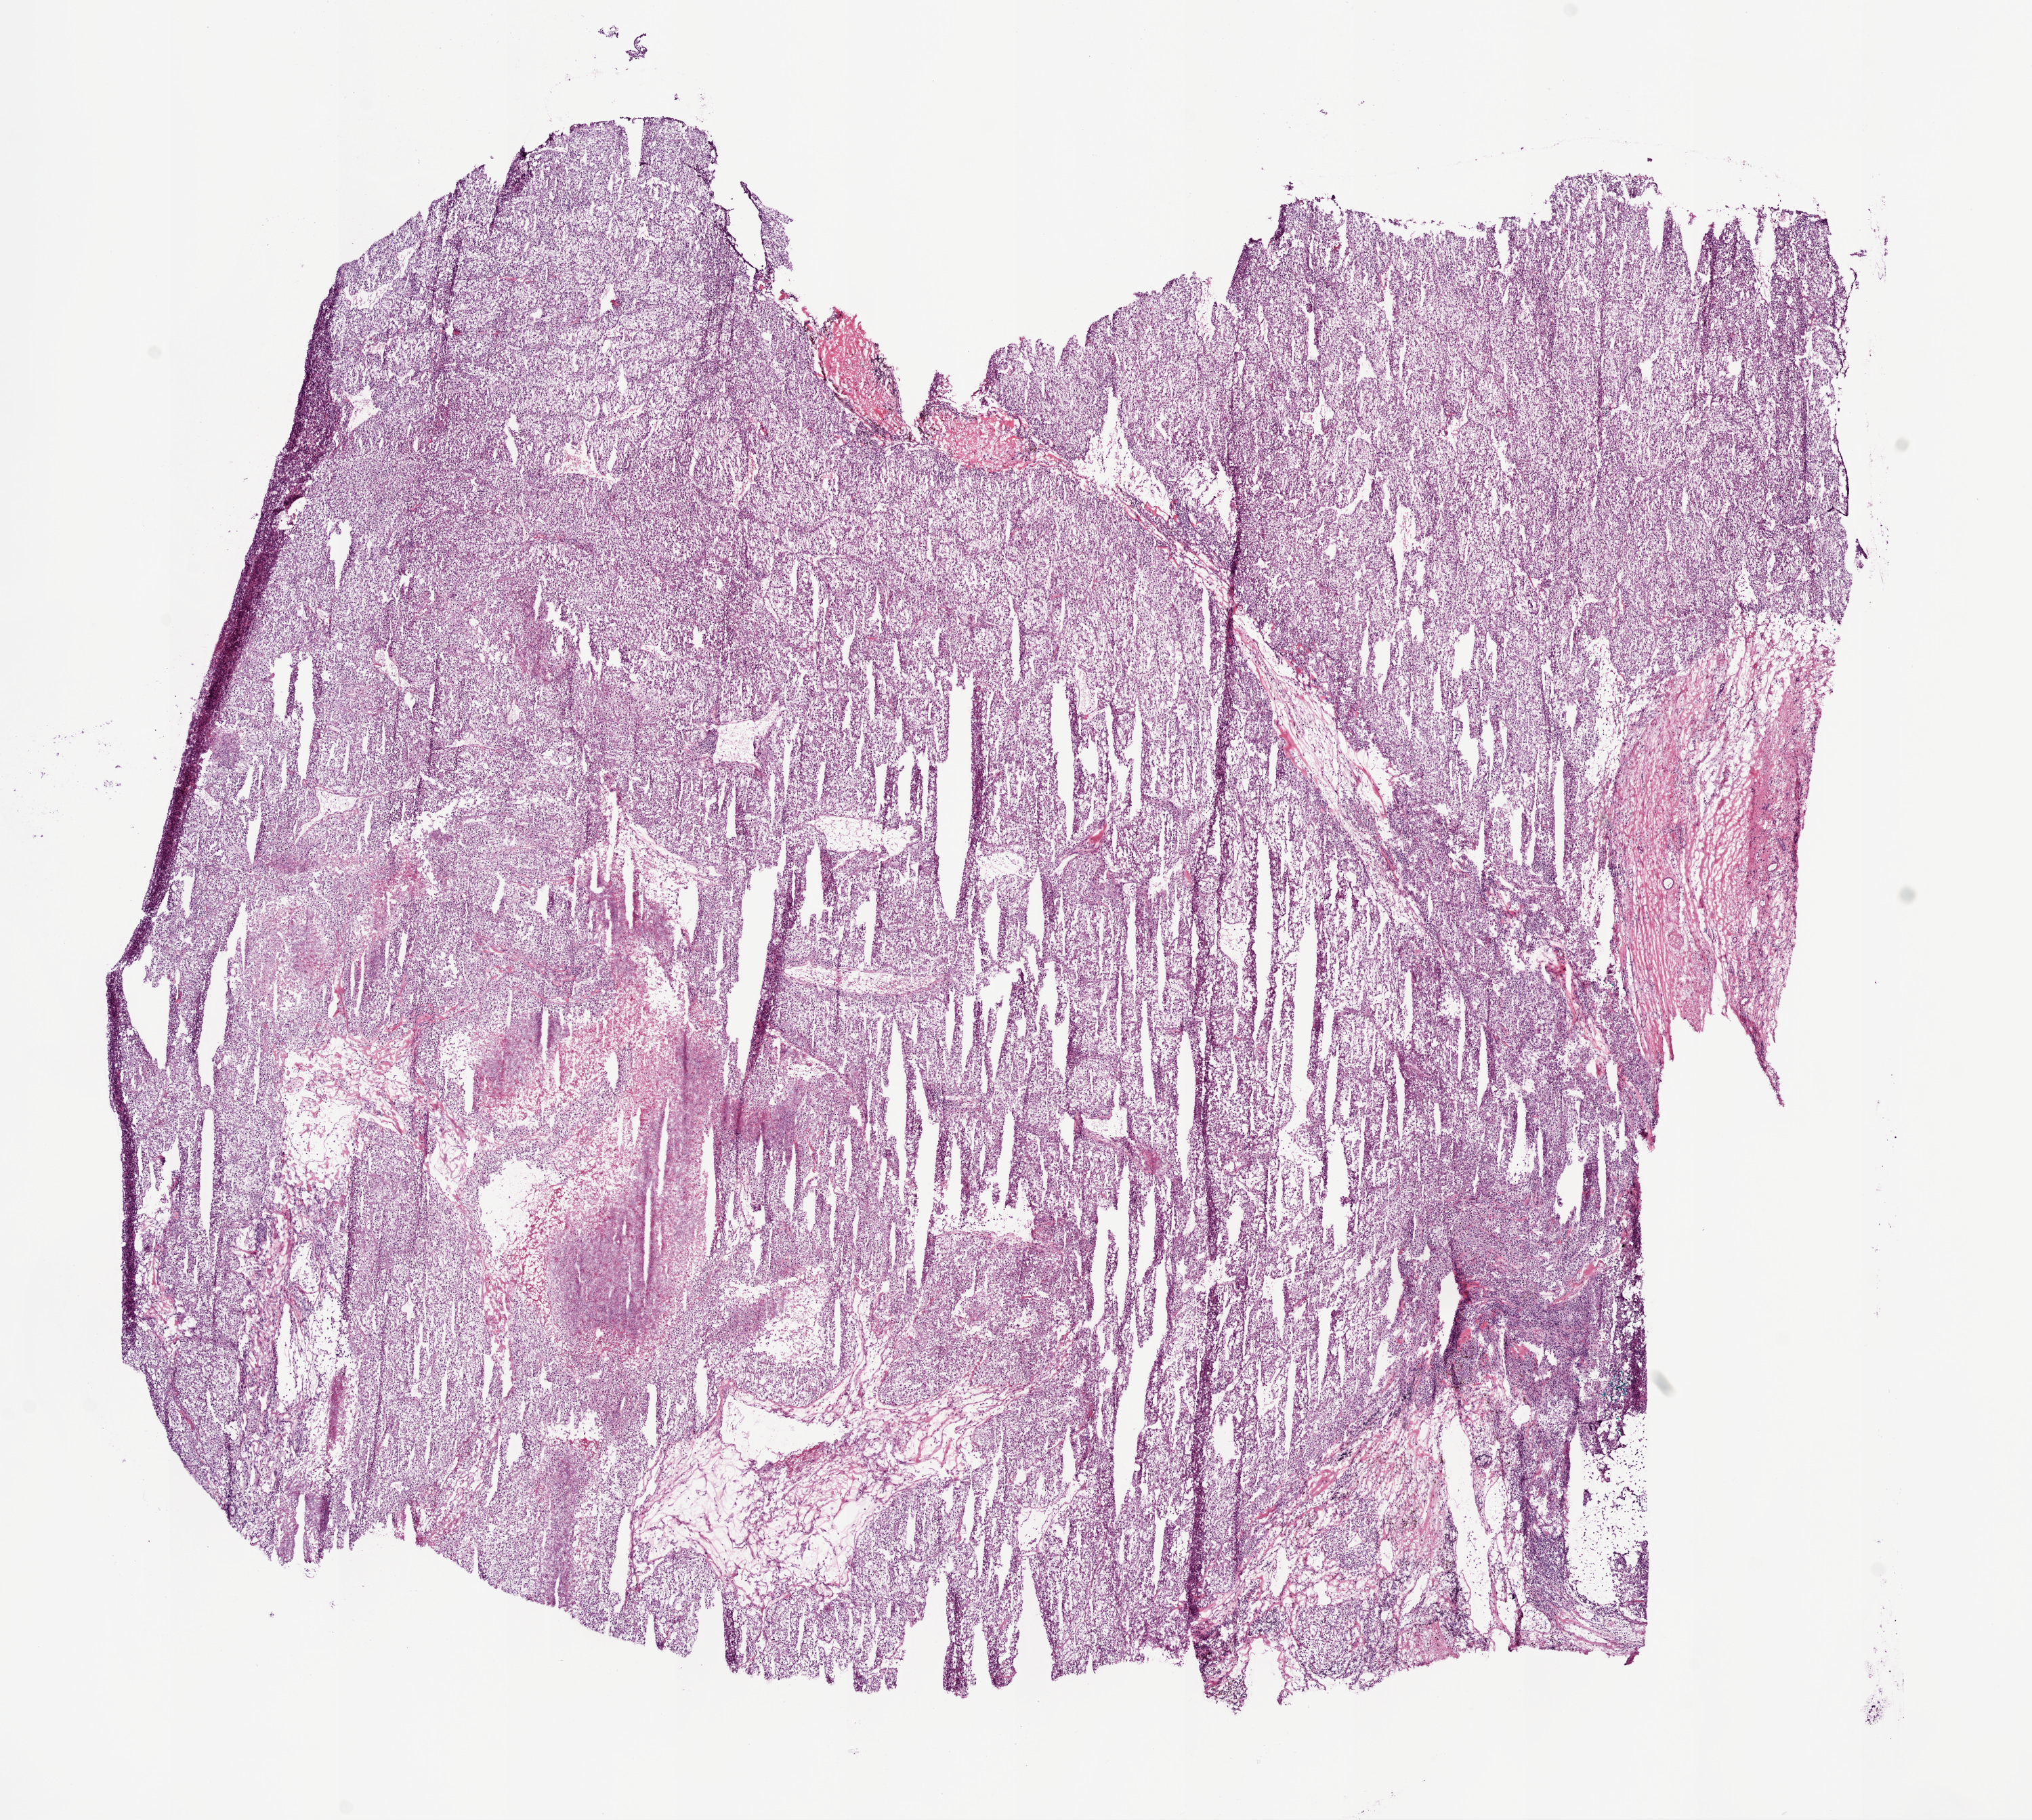
Whole-slide histology image, H&E — low-resolution overview of the scanned area, about 12.0 x 10.8 mm (from a 20x scan); frozen section from the bottom of the tissue portion; sample: primary tumour, kidney. Patient: male, age at initial diagnosis 60 years. Histologic grade: G3 (poorly differentiated). Slide review estimates, as recorded: tumour cells 95%, tumour nuclei 90%, normal cells 0%, stromal cells 5%, necrosis 0%.
Laterality: left. Diagnosis: Clear cell adenocarcinoma, NOS. AJCC pathologic stage: I.